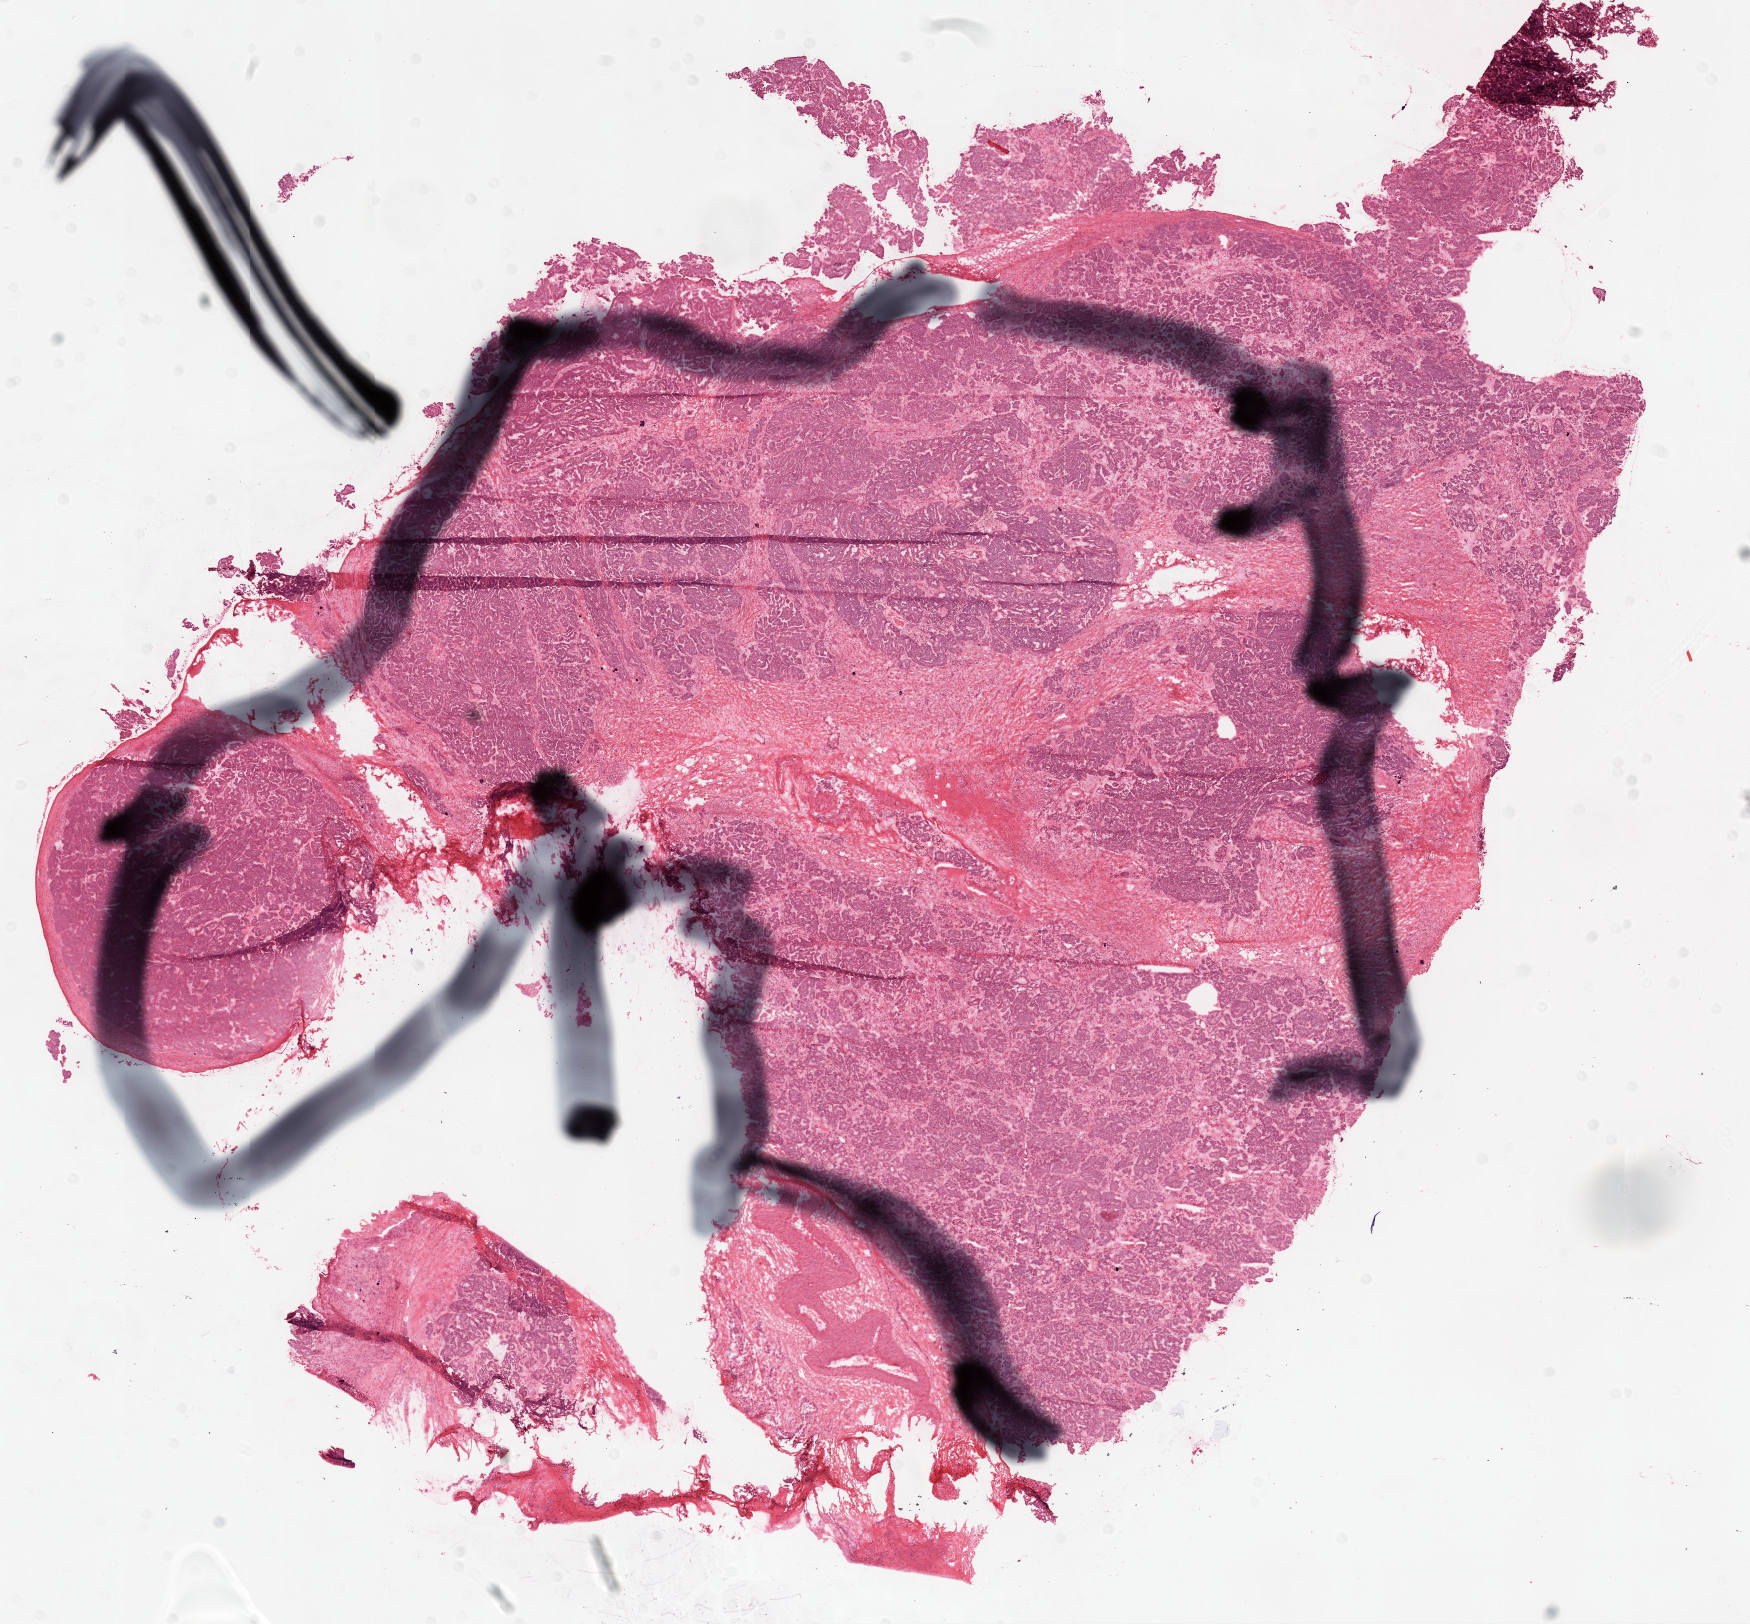
Whole-slide histology image, H&E — whole scanned area (about 14.0 x 13.0 mm, acquisition: 20x scan) shown as a low-resolution overview; frozen section from the top of the tissue portion; primary tumour sample from the ovary. Patient: female, age at initial diagnosis 40 years. Histologic grade: G3 (poorly differentiated). Pathologist review of this section (percent, as recorded): tumour cells 80%, tumour nuclei 90%, normal cells 0%, stromal cells 0%, necrosis 20%.
FIGO stage: IIIC. Histologic diagnosis: Serous cystadenocarcinoma, NOS.